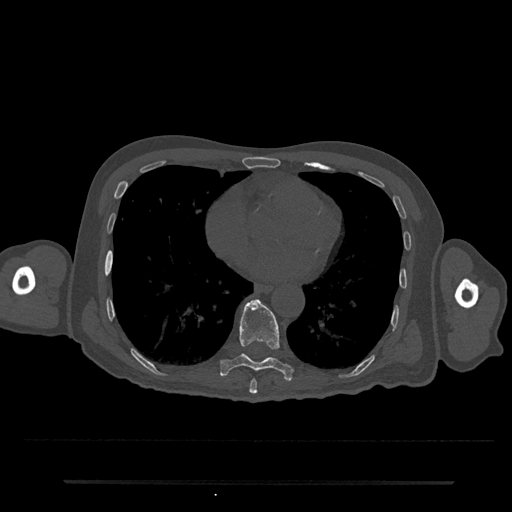
CT including the spine, one axial slice. Position 369 of 797 along the scan axis. Bone window (W 1800 / L 400 HU). 512 × 512 image matrix. Patient: male, 74 years. From the clinical record (not read from this slice): primary cancer: prostate.
Outlined on this slice (semi-automatically segmented with operator editing):
- T8 vertebra: box from (x=249, y=379) to (x=258, y=394) px
- T9 vertebra: (x=220, y=299)–(x=294, y=380)